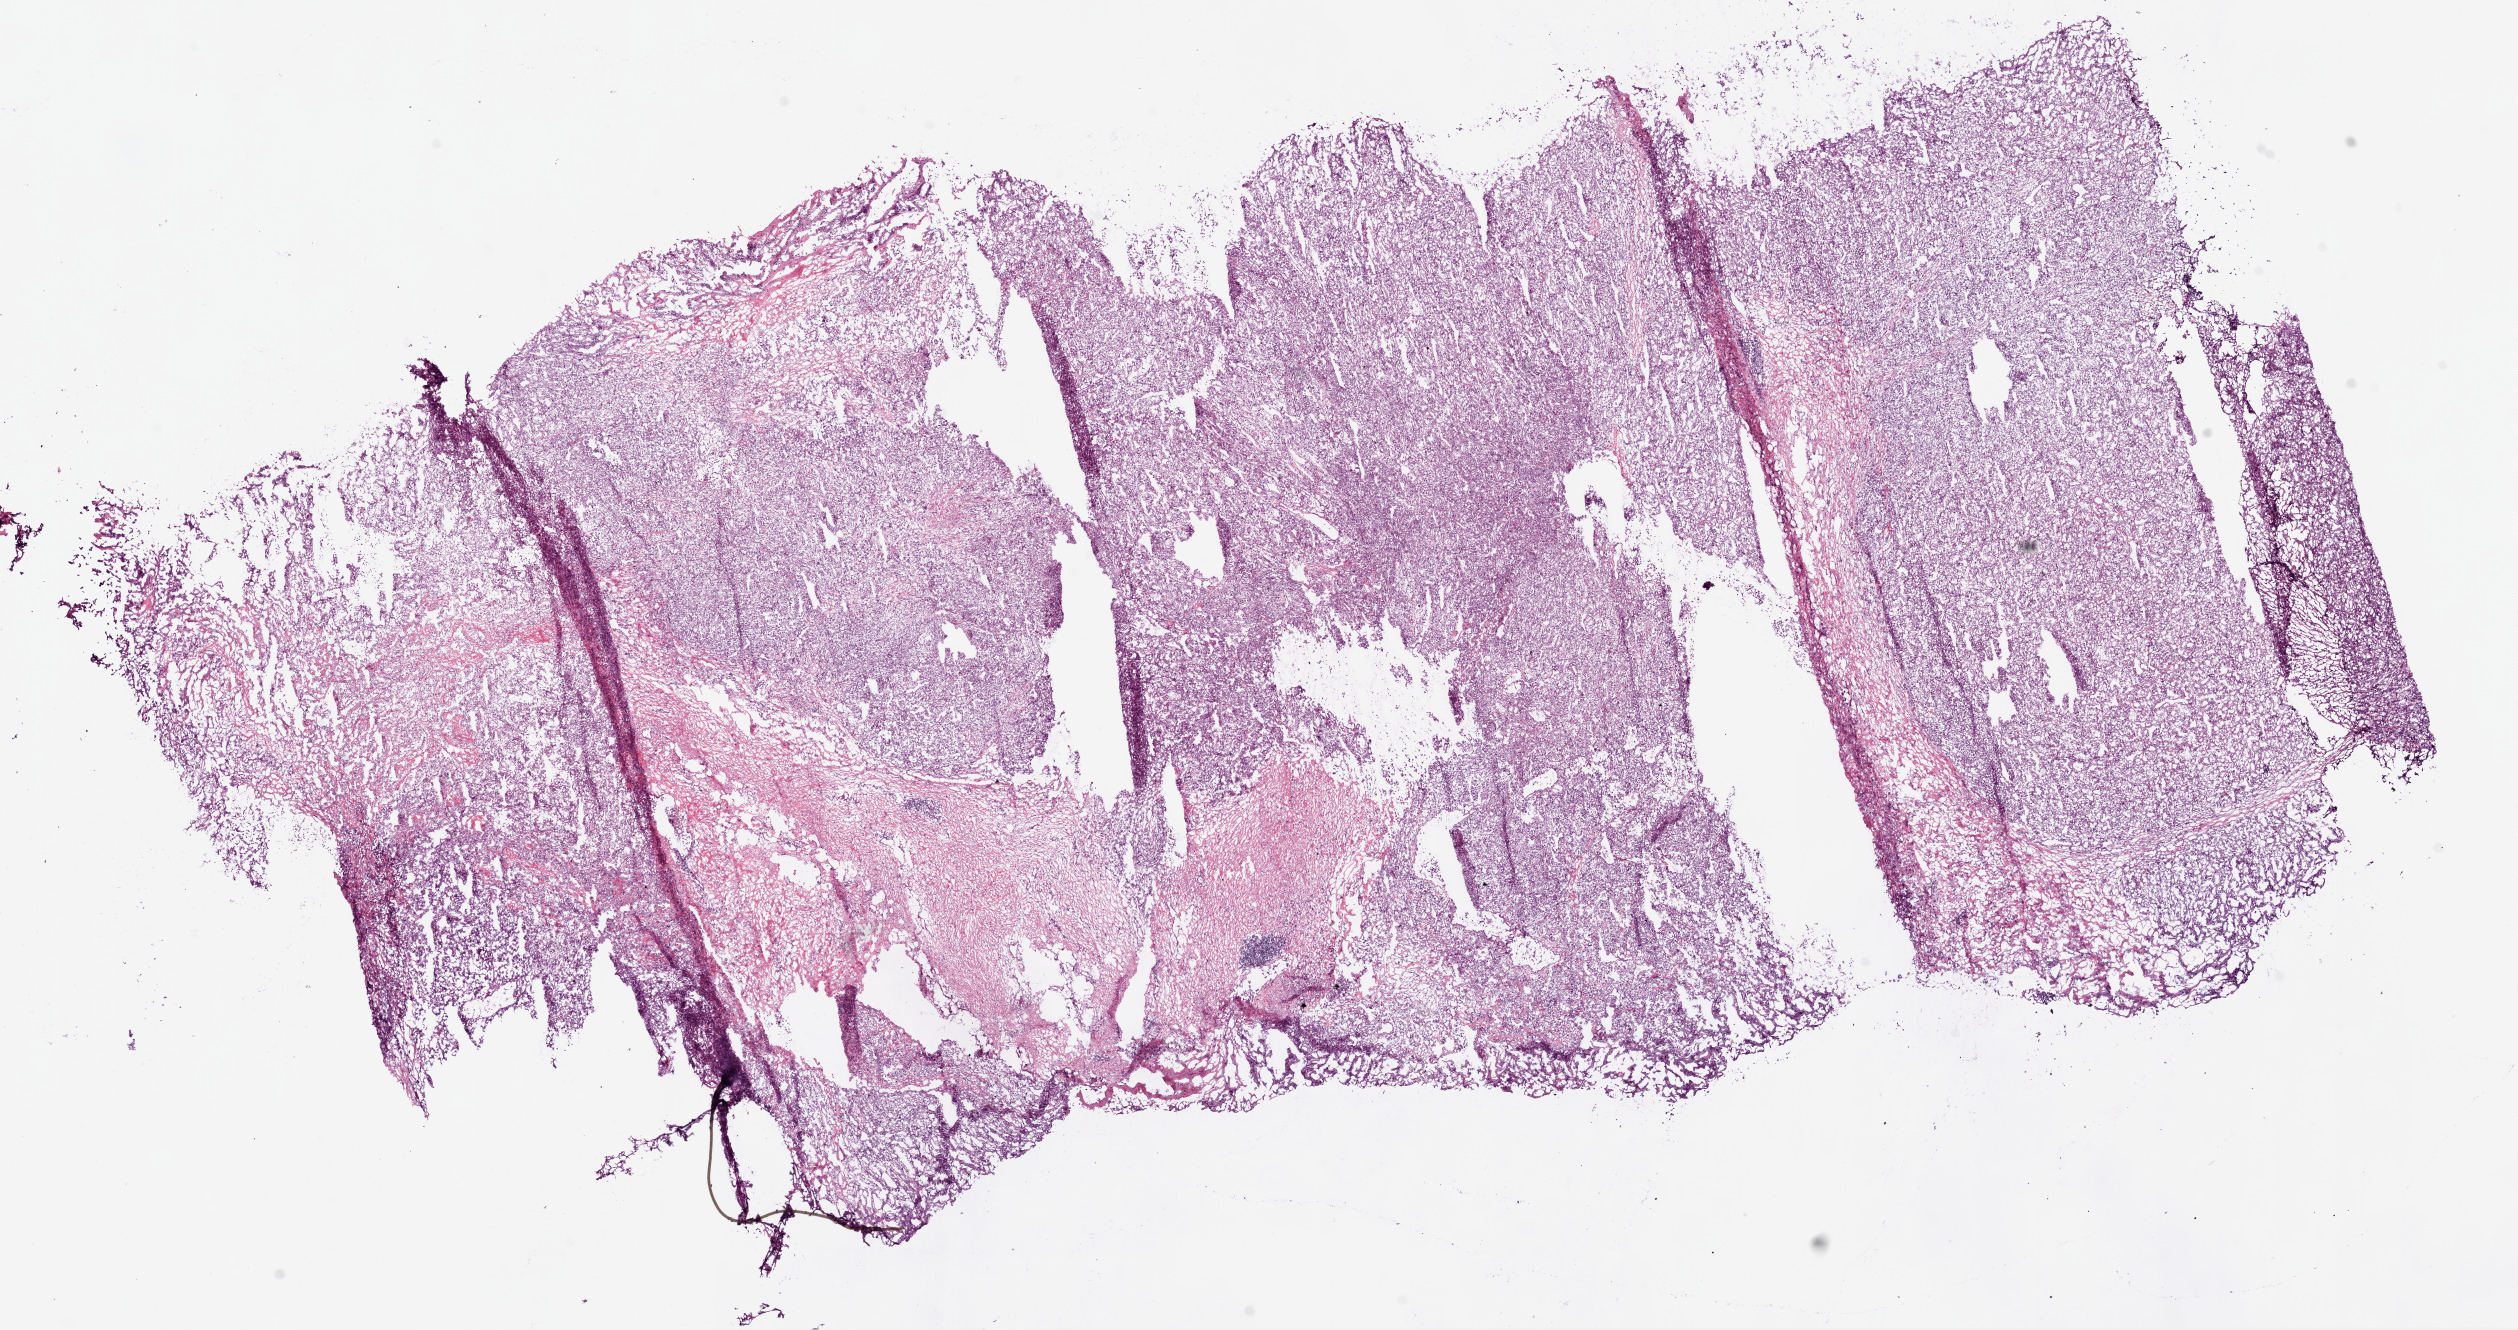
H&E-stained whole-slide image, shown as a low-resolution overview of the whole scanned area (about 20.3 x 10.7 mm). Frozen section from the top of the tissue portion. Sample: primary tumour, kidney. Female, age 54 years at initial diagnosis. Histologic grade: G4 (undifferentiated). Composition of this section per pathologist review: tumour cells 80%, tumour nuclei 80%, normal cells 0%, stromal cells 20%, necrosis 0%. Inflammatory infiltration, as recorded: lymphocyte infiltration 5%, monocyte infiltration 0%, neutrophil infiltration 0%.
• diagnosis: Clear cell adenocarcinoma, NOS
• laterality: right
• AJCC pathologic stage: IV